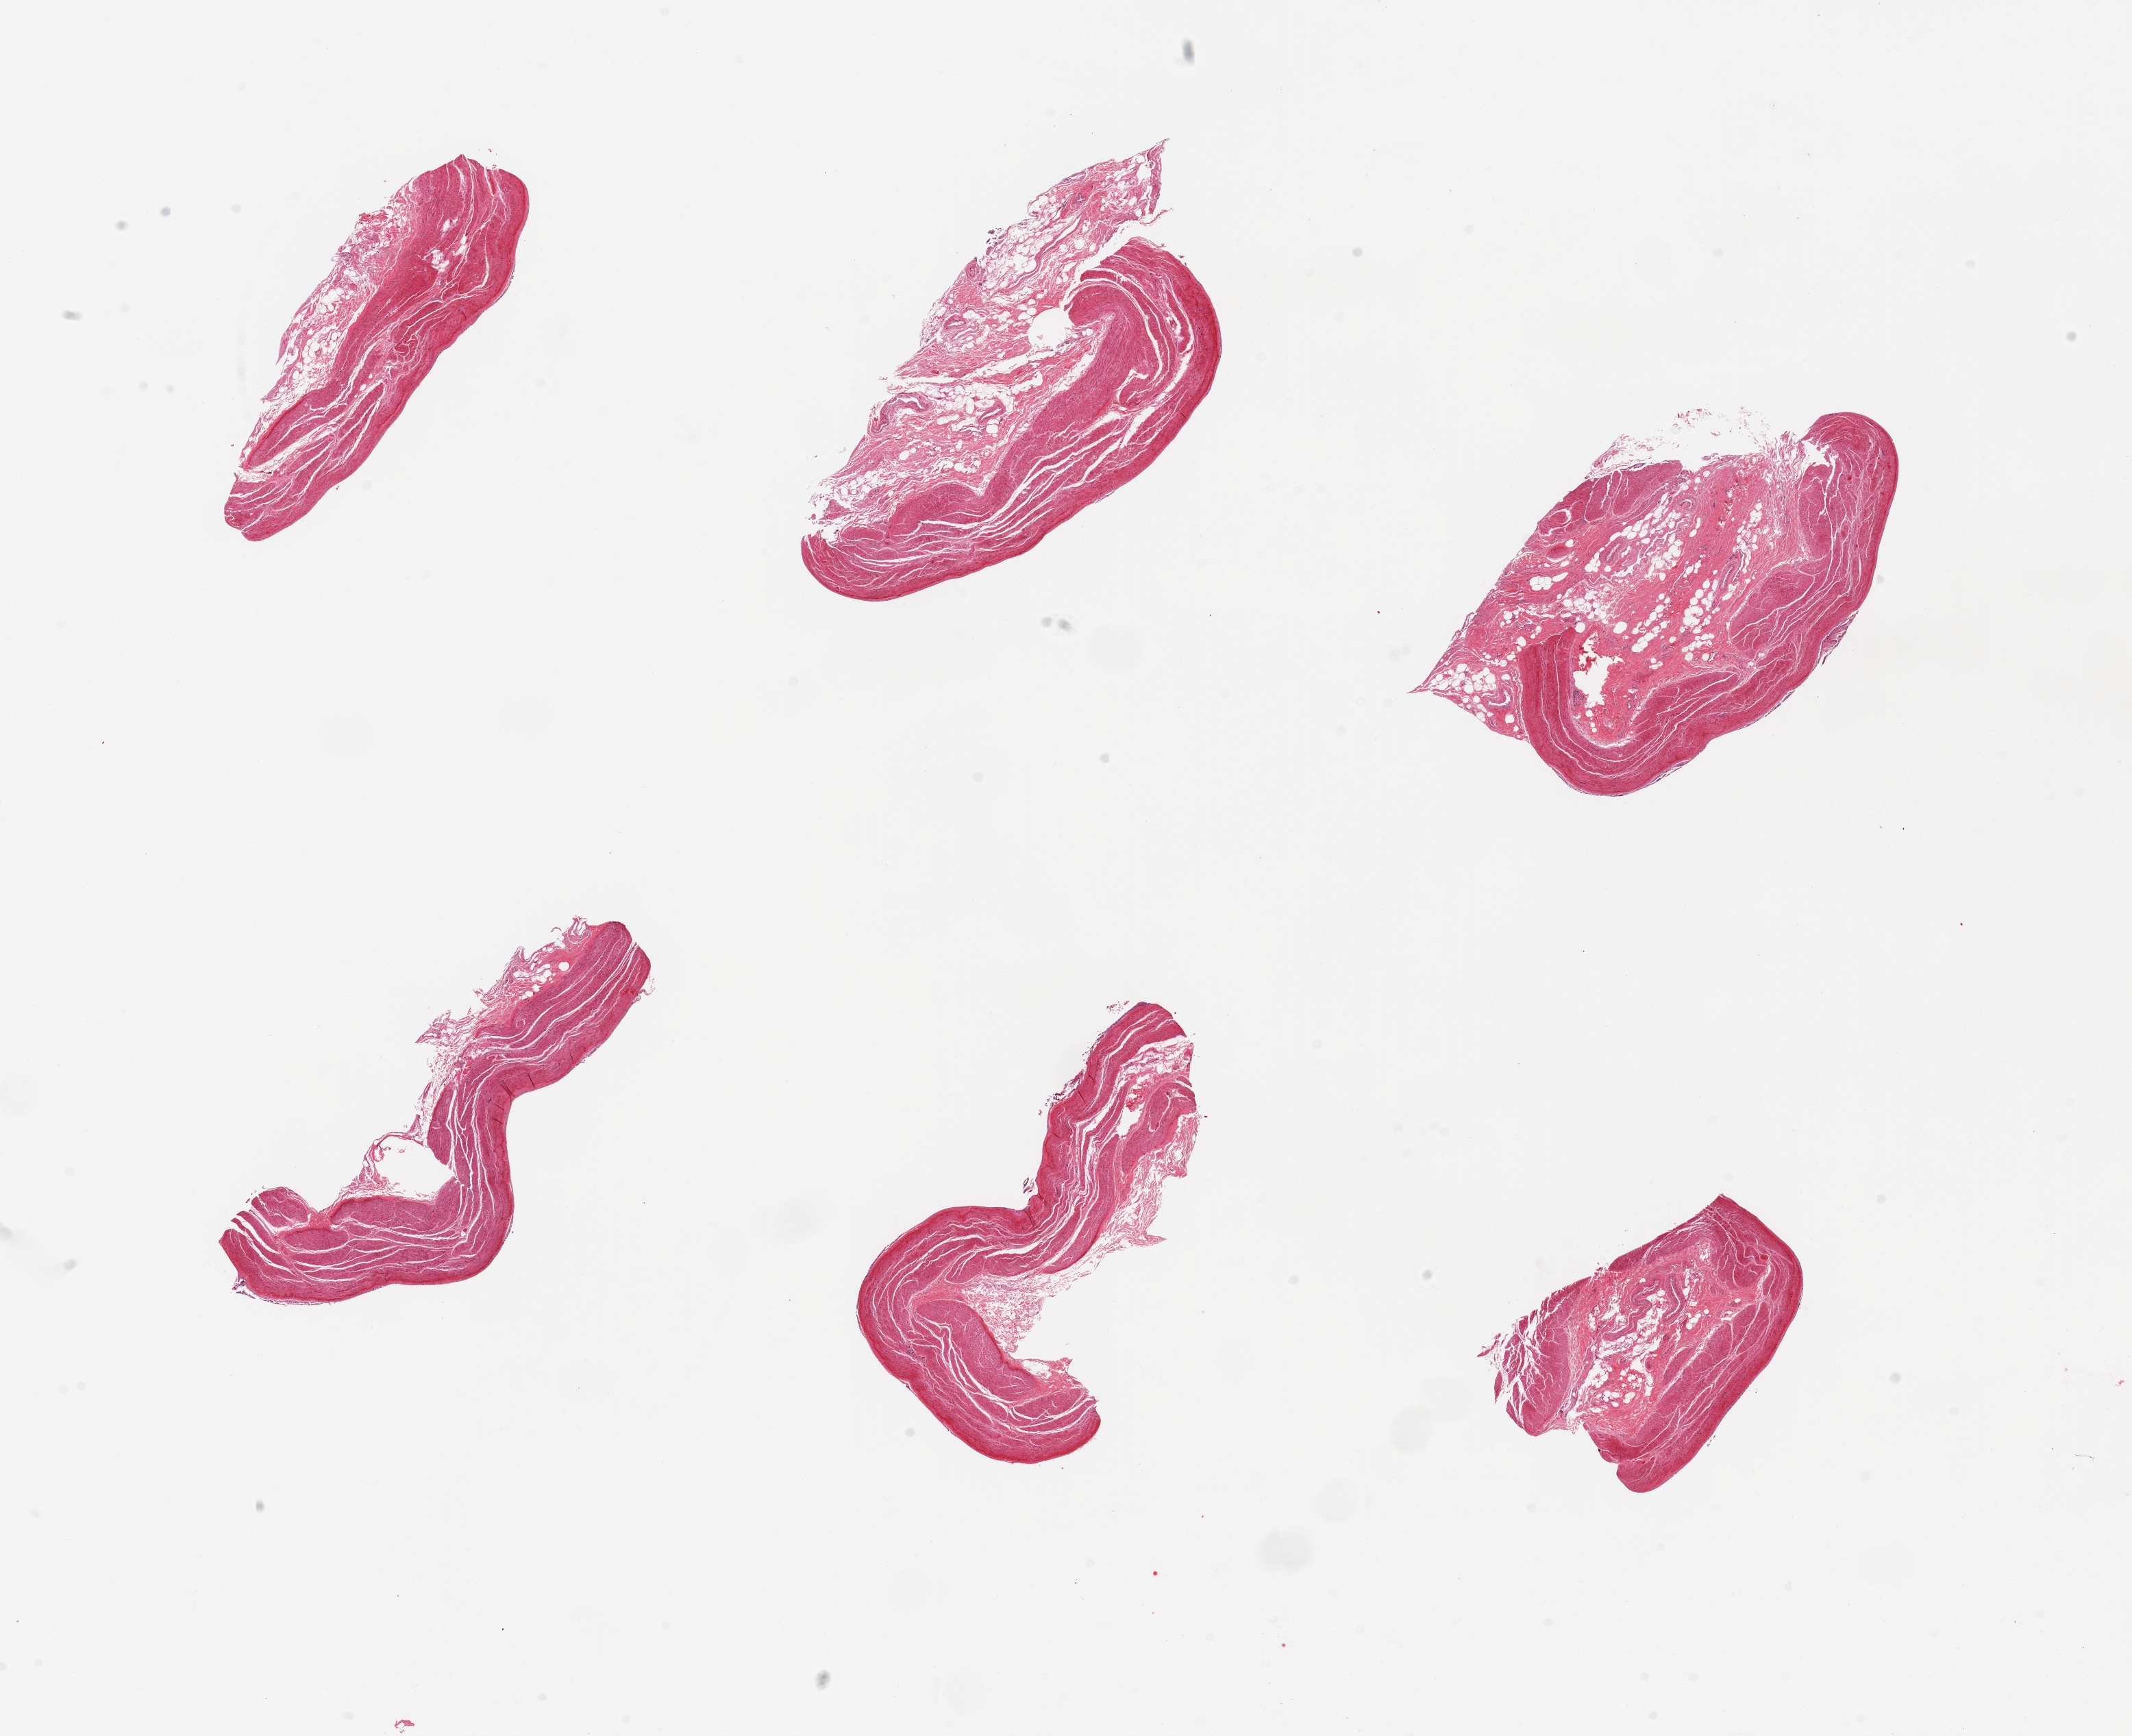
Hematoxylin and eosin (H&E) whole-slide image, low-resolution overview of the scanned area, about 24.6 x 20.0 mm (slide scanned at 20x), PAXgene-fixed, paraffin-embedded tissue, sampled site (target tissue): stomach, donor tissue sample. Male donor.
Pathologist's review note for this sample: 6 pieces; only muscularis present; NO MUCOSA.